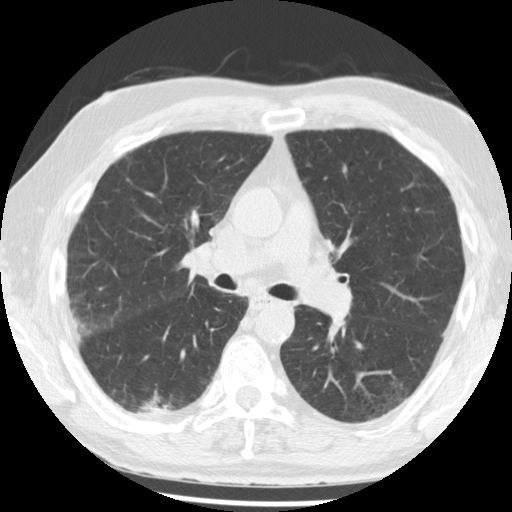
Low-dose screening chest CT, one axial slice; slice 123 of 221 in the series (ordered by position); 120 kVp; lung window (W 1500 / L -600 HU); 2.5 mm slice thickness; 512 × 512 image matrix, field of view 350 × 350 mm.
Outlined on this slice (outlined manually by an expert reader):
- lesion 1 (tumor, lower lobe of right lung): box from (x=137, y=391) to (x=180, y=418) px